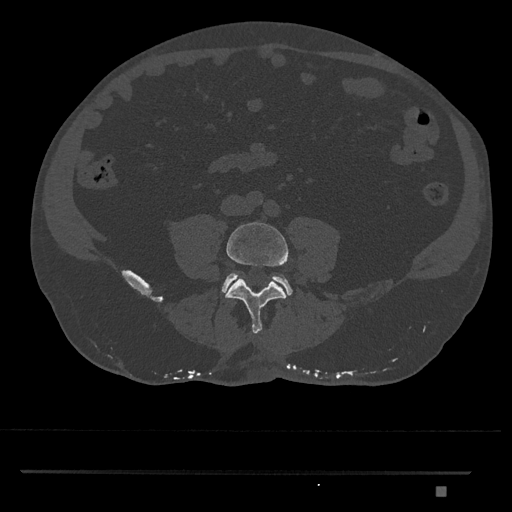
CT including the spine, one axial slice; position 599 of 1134 along the scan axis; reconstruction kernel Br40s/3; bone window (W 1800 / L 400 HU); 0.5 mm slice thickness; 512 × 512 image matrix, field of view 429 × 429 mm. Patient: male, 65 years. From the clinical record (not read from this slice): primary cancer: prostate.
Outlined on this slice (semi-automatic segmentation, software-assisted and operator-edited):
- L4 vertebra: box from (x=225, y=222) to (x=288, y=334) px
- L5 vertebra: (x=222, y=273)–(x=292, y=296)